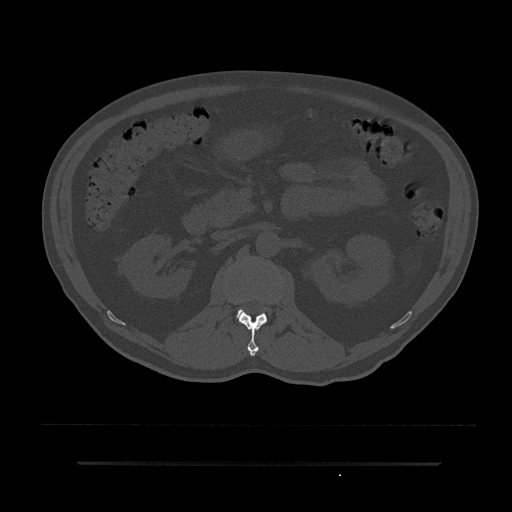
CT including the spine, one axial slice. Position 116 of 797 along the scan axis. Reconstruction kernel Br40s/3. 120 kVp. Bone window (W 1800 / L 400 HU). 0.5 mm slice thickness. 512 × 512 image matrix, field of view 464 × 464 mm. Male patient, age 59 years. From the clinical record (not read from this slice): primary cancer: bile ducts; vertebrae with lytic lesions (as recorded): T10.
Structures marked on this image (semi-automatically segmented with operator editing):
- L1 vertebra: bounding box <239,298,267,356> (left, top, right, bottom; pixels)
- L2 vertebra: <237,309,267,322>